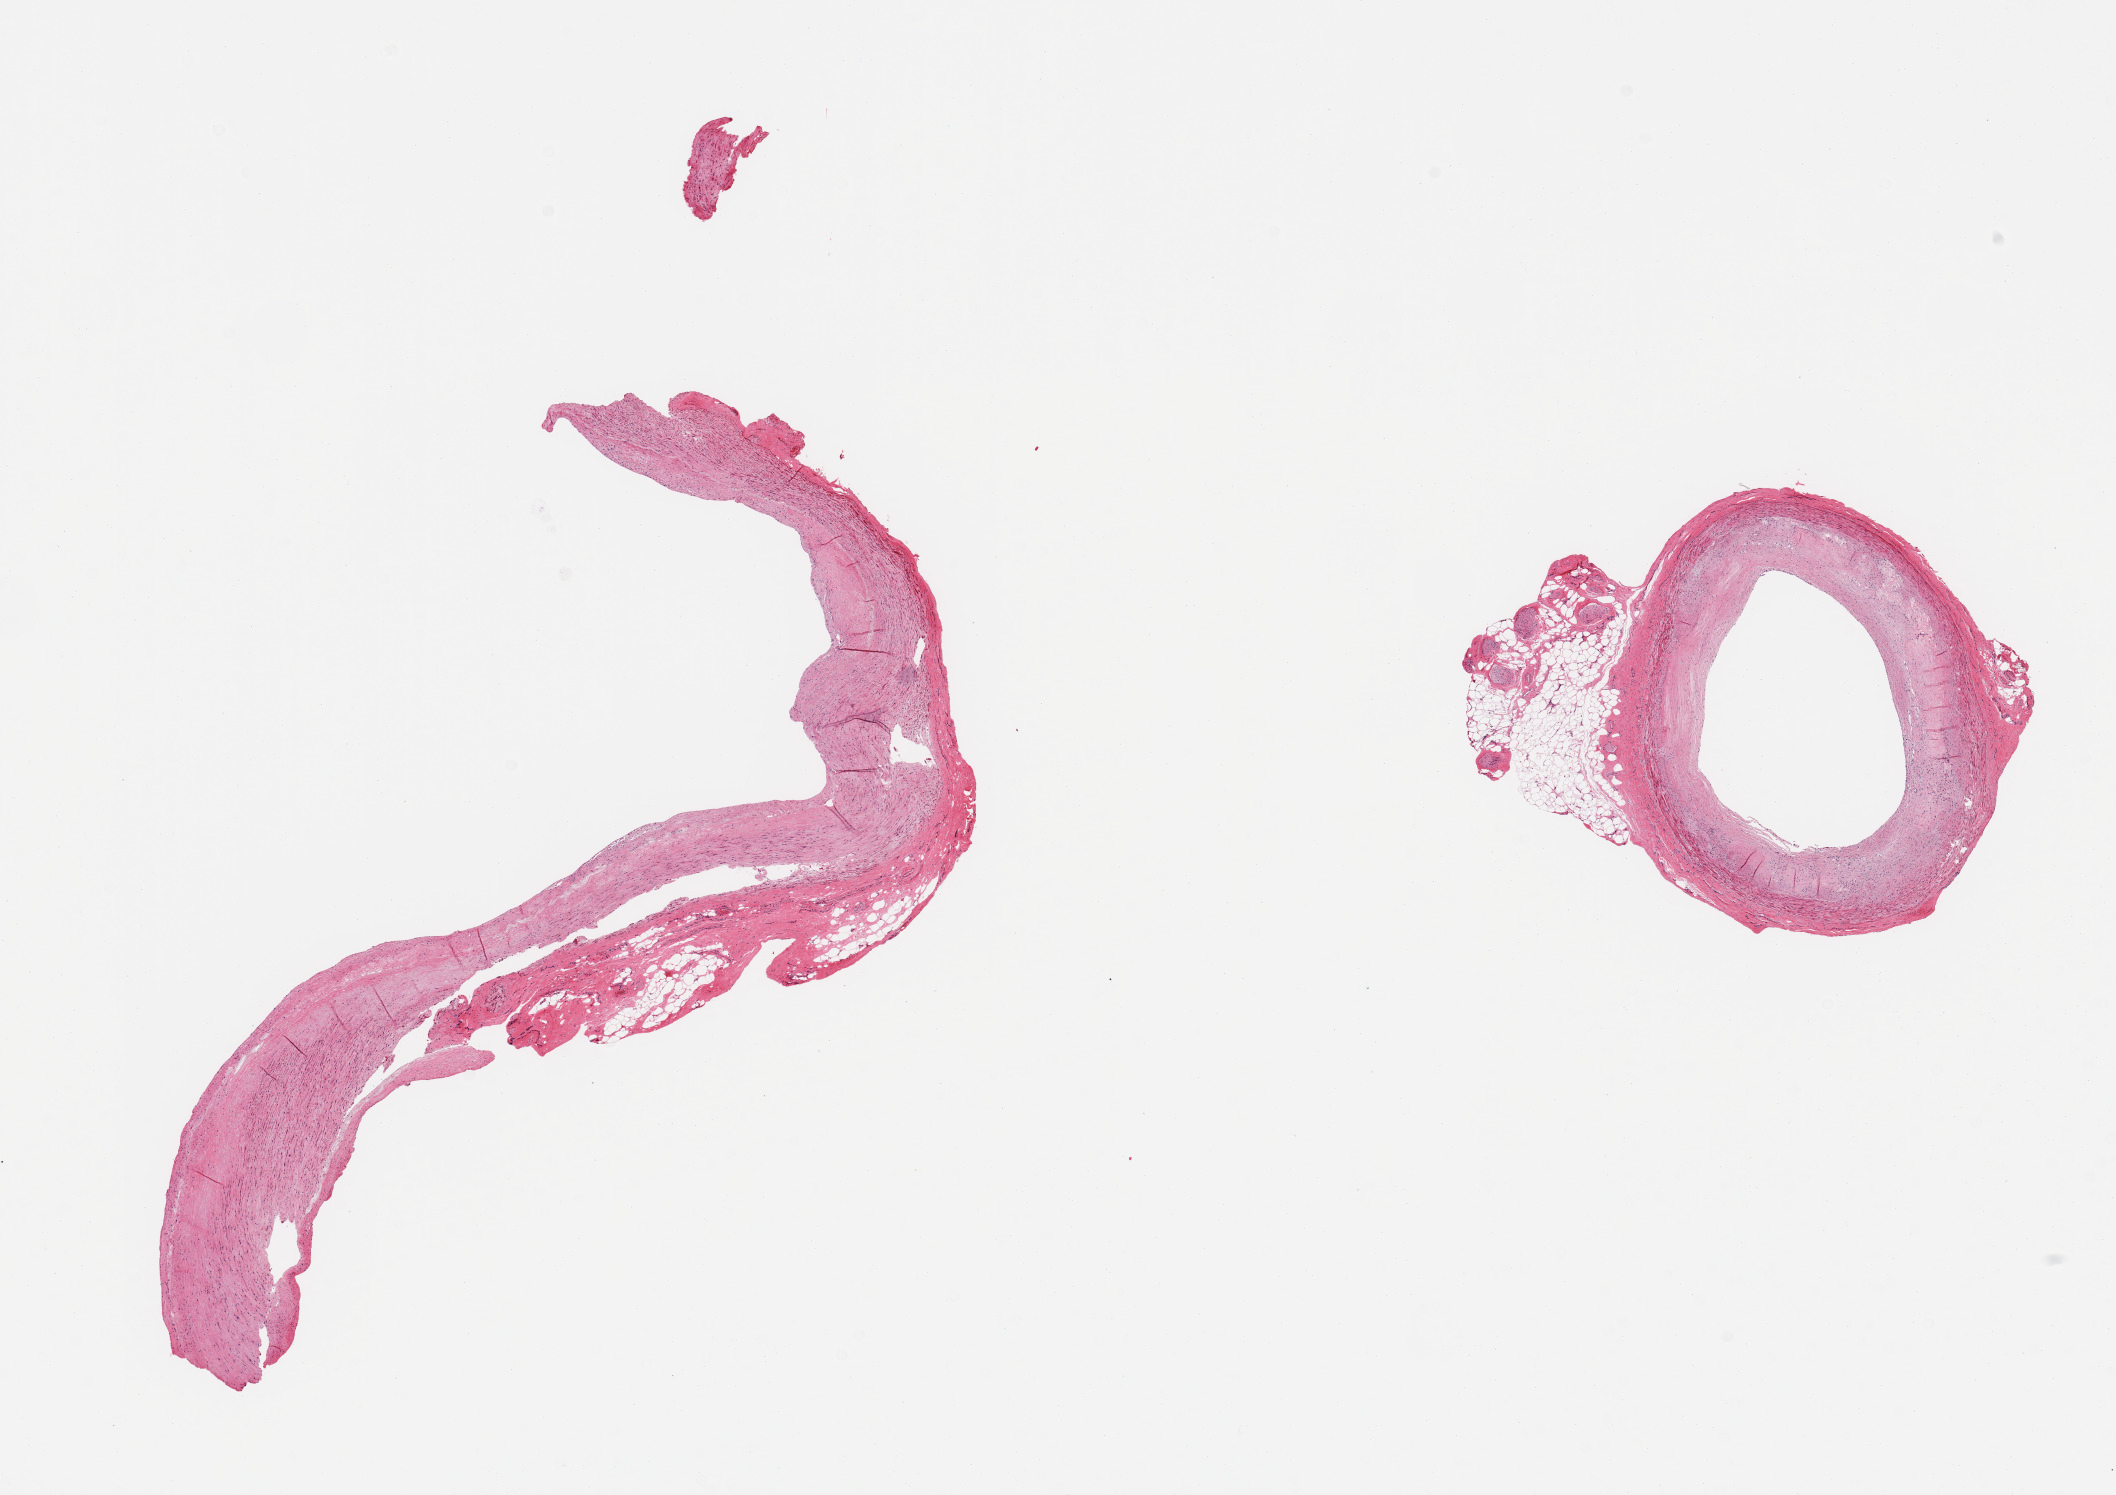
Hematoxylin and eosin (H&E) whole-slide image — whole scanned area (about 16.7 x 11.8 mm, slide scanned at 20x) shown as a low-resolution overview, PAXgene-fixed, paraffin-embedded tissue, sampled site (target tissue): coronary artery, donor tissue sample. Donor sex: male.
• review note (as recorded): 2 pieces; atherosclerosis, attachment of fat/nerve